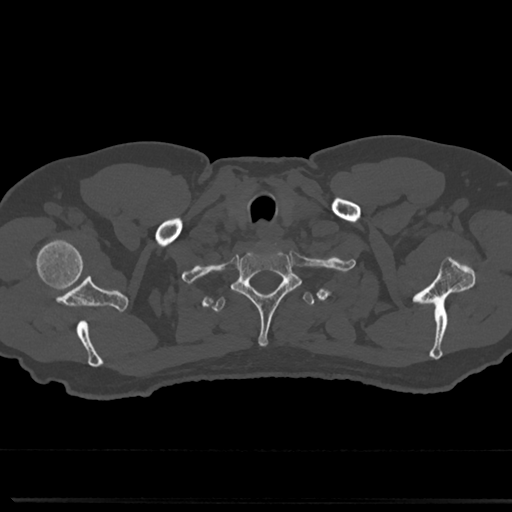
CT including the spine, one axial slice; position 669 of 817 along the scan axis; bone window (W 1800 / L 400 HU); 0.5 mm slice thickness; 512 × 512 image matrix, field of view 355 × 355 mm. Patient: male, 61 years. From the clinical record (not read from this slice): primary cancer: prostate.
Annotated regions visible in this slice (semi-automatically segmented with operator editing):
- T1 vertebra: bounding box [x1, y1, x2, y2] px = [233, 247, 299, 345]
- T2 vertebra: [212, 291, 315, 315]